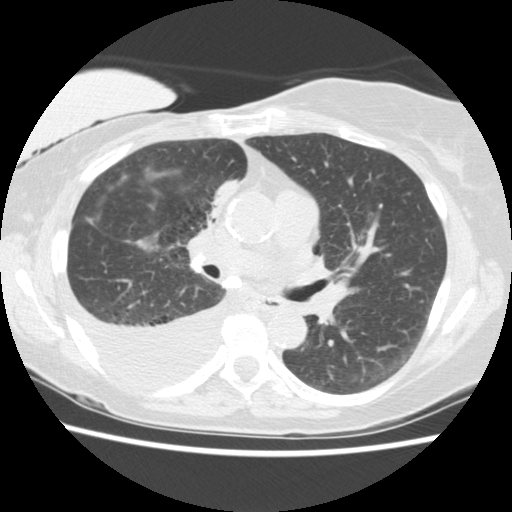
Chest CT (low-dose screening protocol), one axial image, third screening round (two years after baseline), lung window (W 1500 / L -600 HU), 2.5 mm slice thickness, 120 kVp. Female participant, aged 56 years at enrolment. Current smoker at enrolment.
• Expert reader's lesion annotation, bounding box <185,167,251,235> (left, top, right, bottom; pixels).
• The screening reader recorded 2 non-calcified nodules or masses ≥4 mm on this exam; which of them this box marks is not recorded.
• Later outcome: lung cancer diagnosed 160 days after this screen — adenocarcinoma, NOS, right upper lobe, stage IIIB (AJCC 6th edition), 8 mm at pathology.